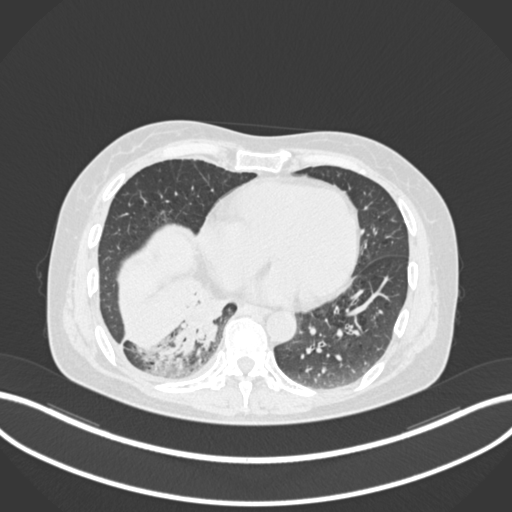
Chest CT, one axial slice. Position 50 of 168 along the scan axis. Reconstruction kernel B30f. 120 kVp. Lung window (W 1500 / L -600 HU). 1 mm slice thickness. 512 × 512 image matrix, field of view 400 × 400 mm. Patient: female, 63 years. Case-level facts recorded for this patient, not image findings: clinical TNM (as recorded): T1c N0 M0.
Outlined on this slice (bounding box drawn by a radiologist):
- lung tumour (recorded histology: adenocarcinoma): bounding box (x1, y1, x2, y2) in pixels: (174, 290, 235, 359)